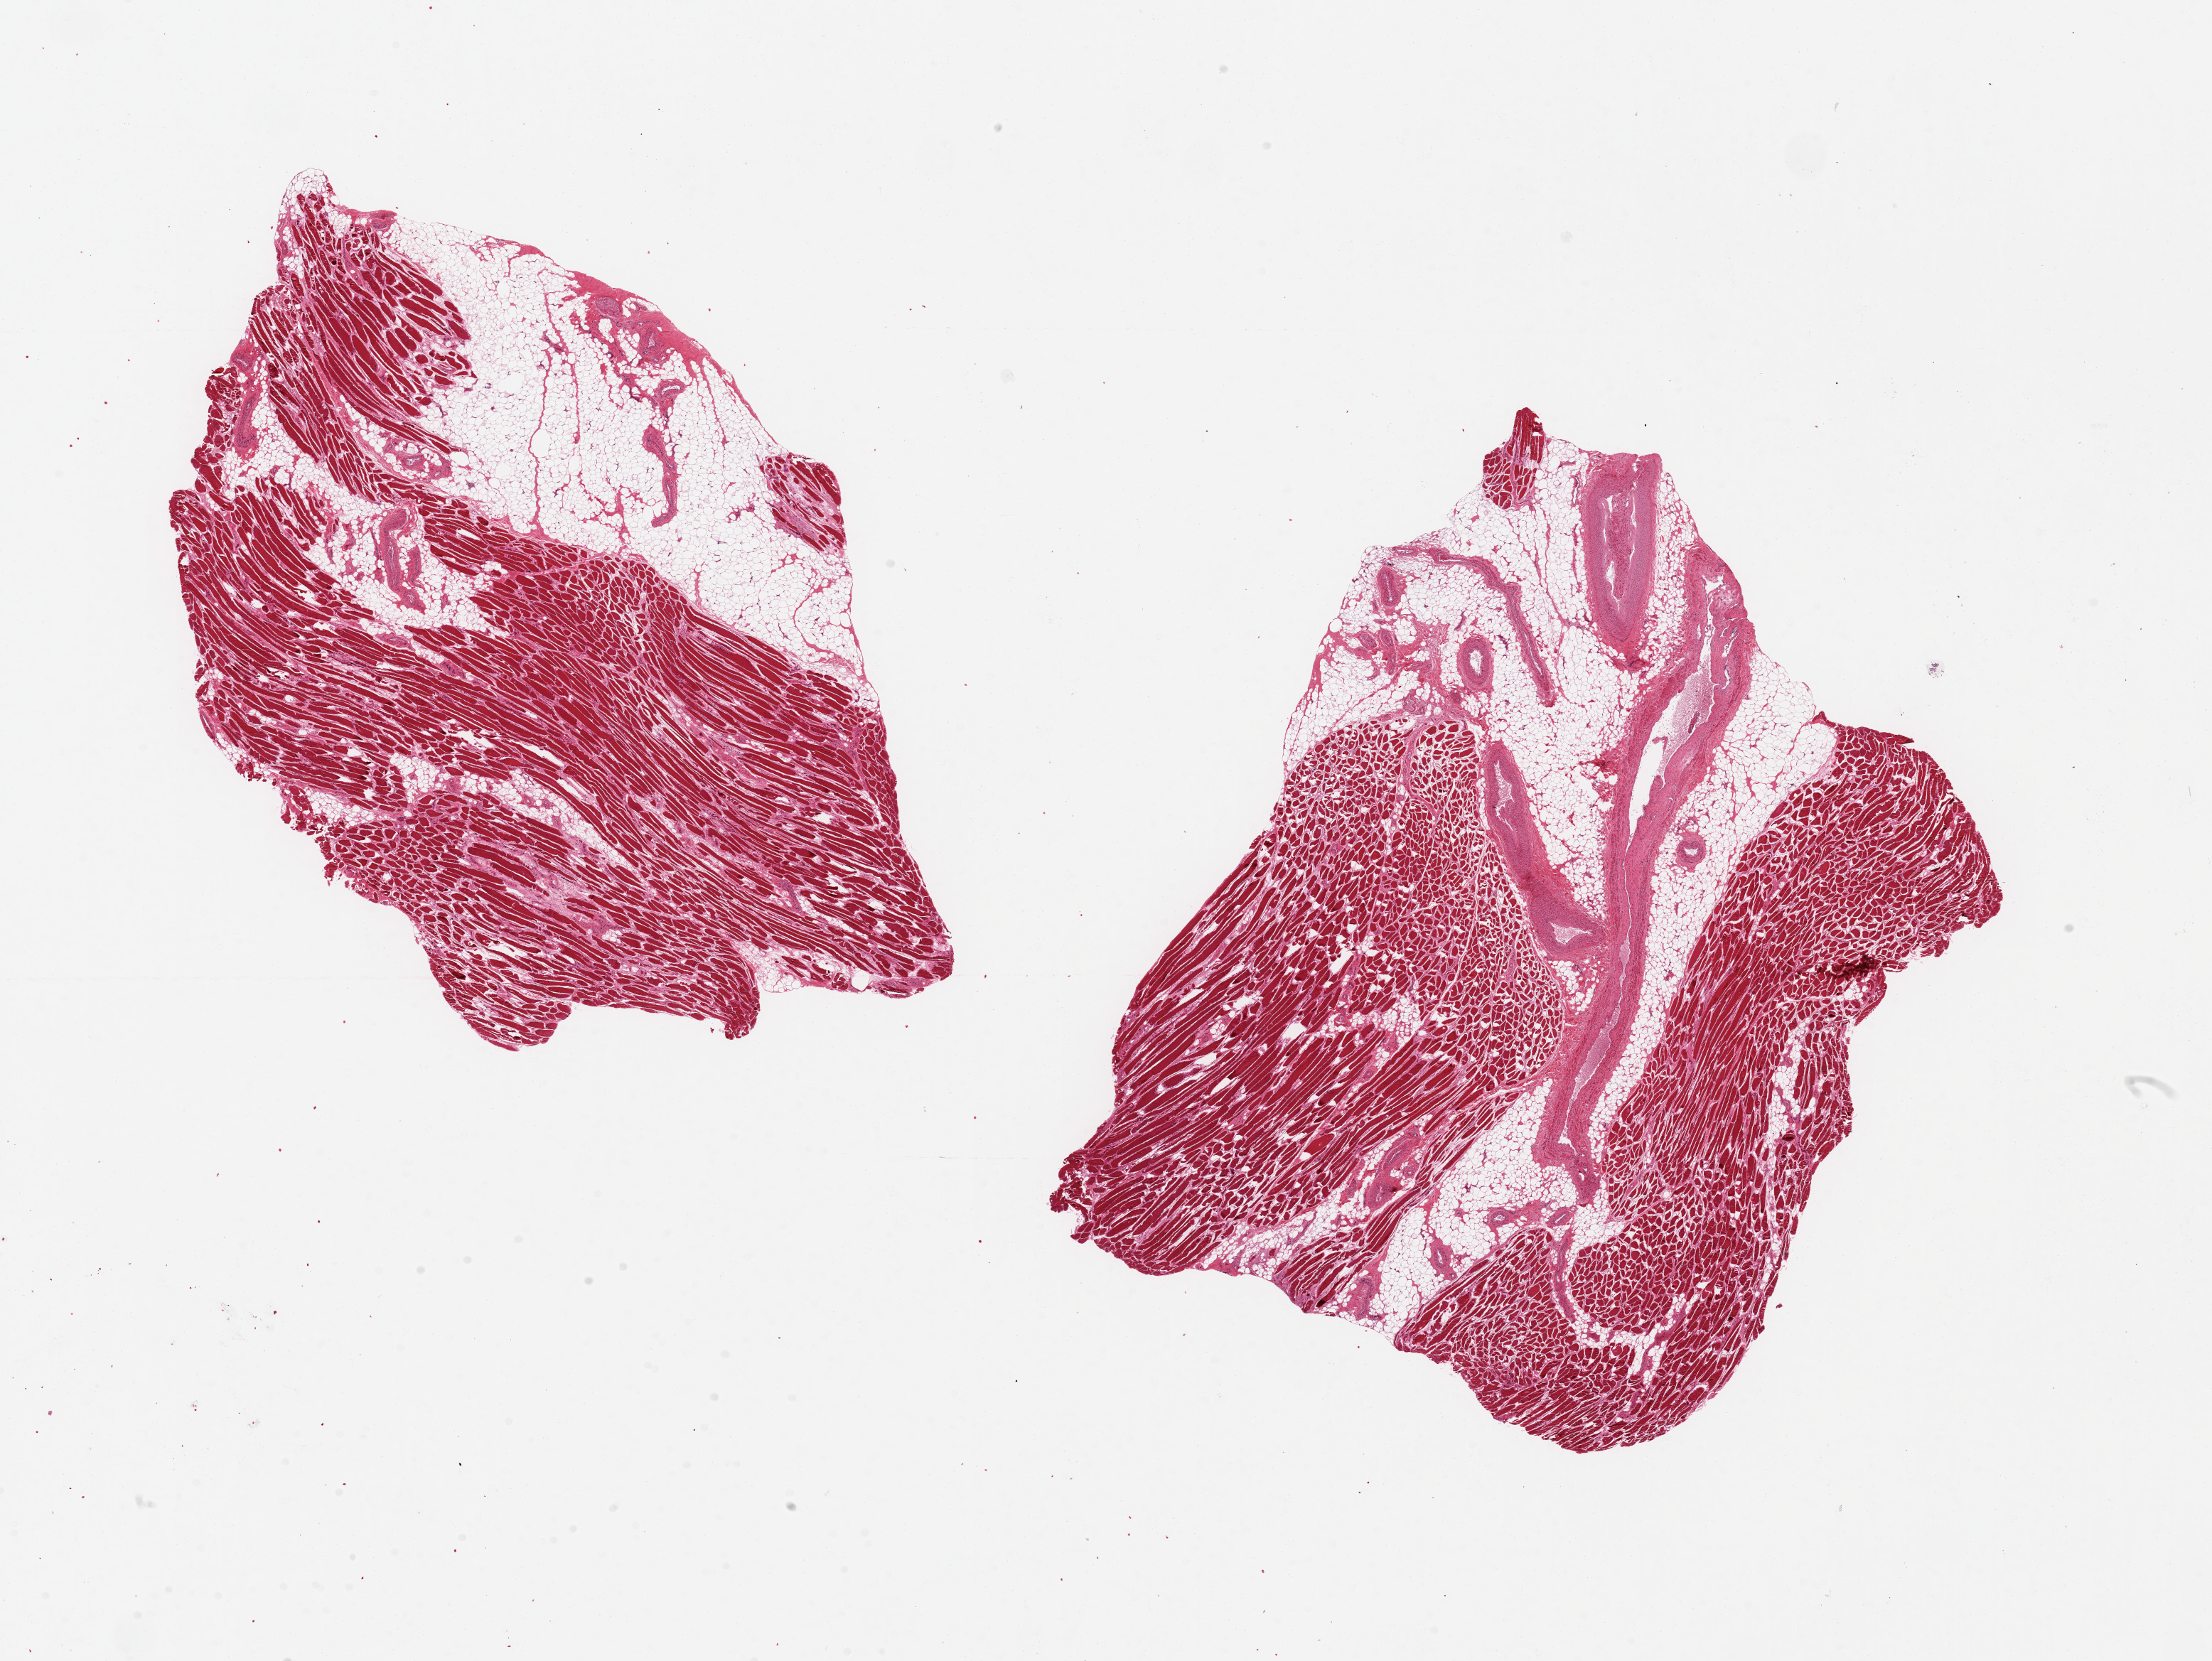
Whole-slide image, haematoxylin and eosin stain, shown as a low-resolution overview of the whole scanned area (about 24.6 x 18.5 mm, from a 20x scan), PAXgene-fixed, paraffin-embedded tissue, section of skeletal muscle (target tissue), donor tissue sample. Male donor.
• pathologist's review note for this sample: 2 pieces 10x7 & 8x8 mm; patchy fibrosis; ~40% adipose in aliquots